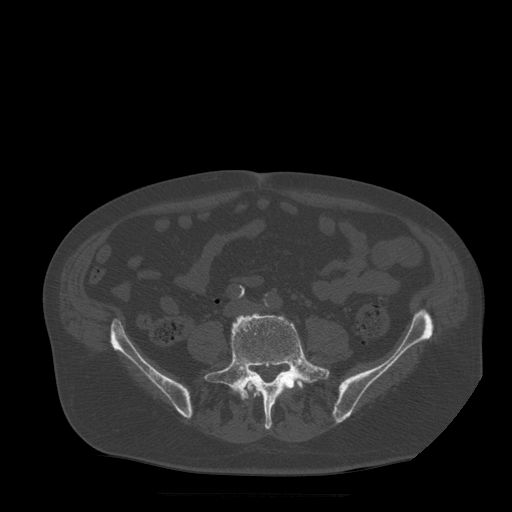
CT including the spine, one axial slice; bone window (W 1800 / L 400 HU); 1.25 mm slice thickness; 512 × 512 image matrix. Patient age 72 years. Case-level facts recorded for this patient, not image findings: primary cancer: prostate.
Annotated regions visible in this slice (semi-automatic segmentation, software-assisted and operator-edited):
- L4 vertebra: box from (x=246, y=380) to (x=293, y=389) px
- L5 vertebra: (x=204, y=313)–(x=330, y=430)